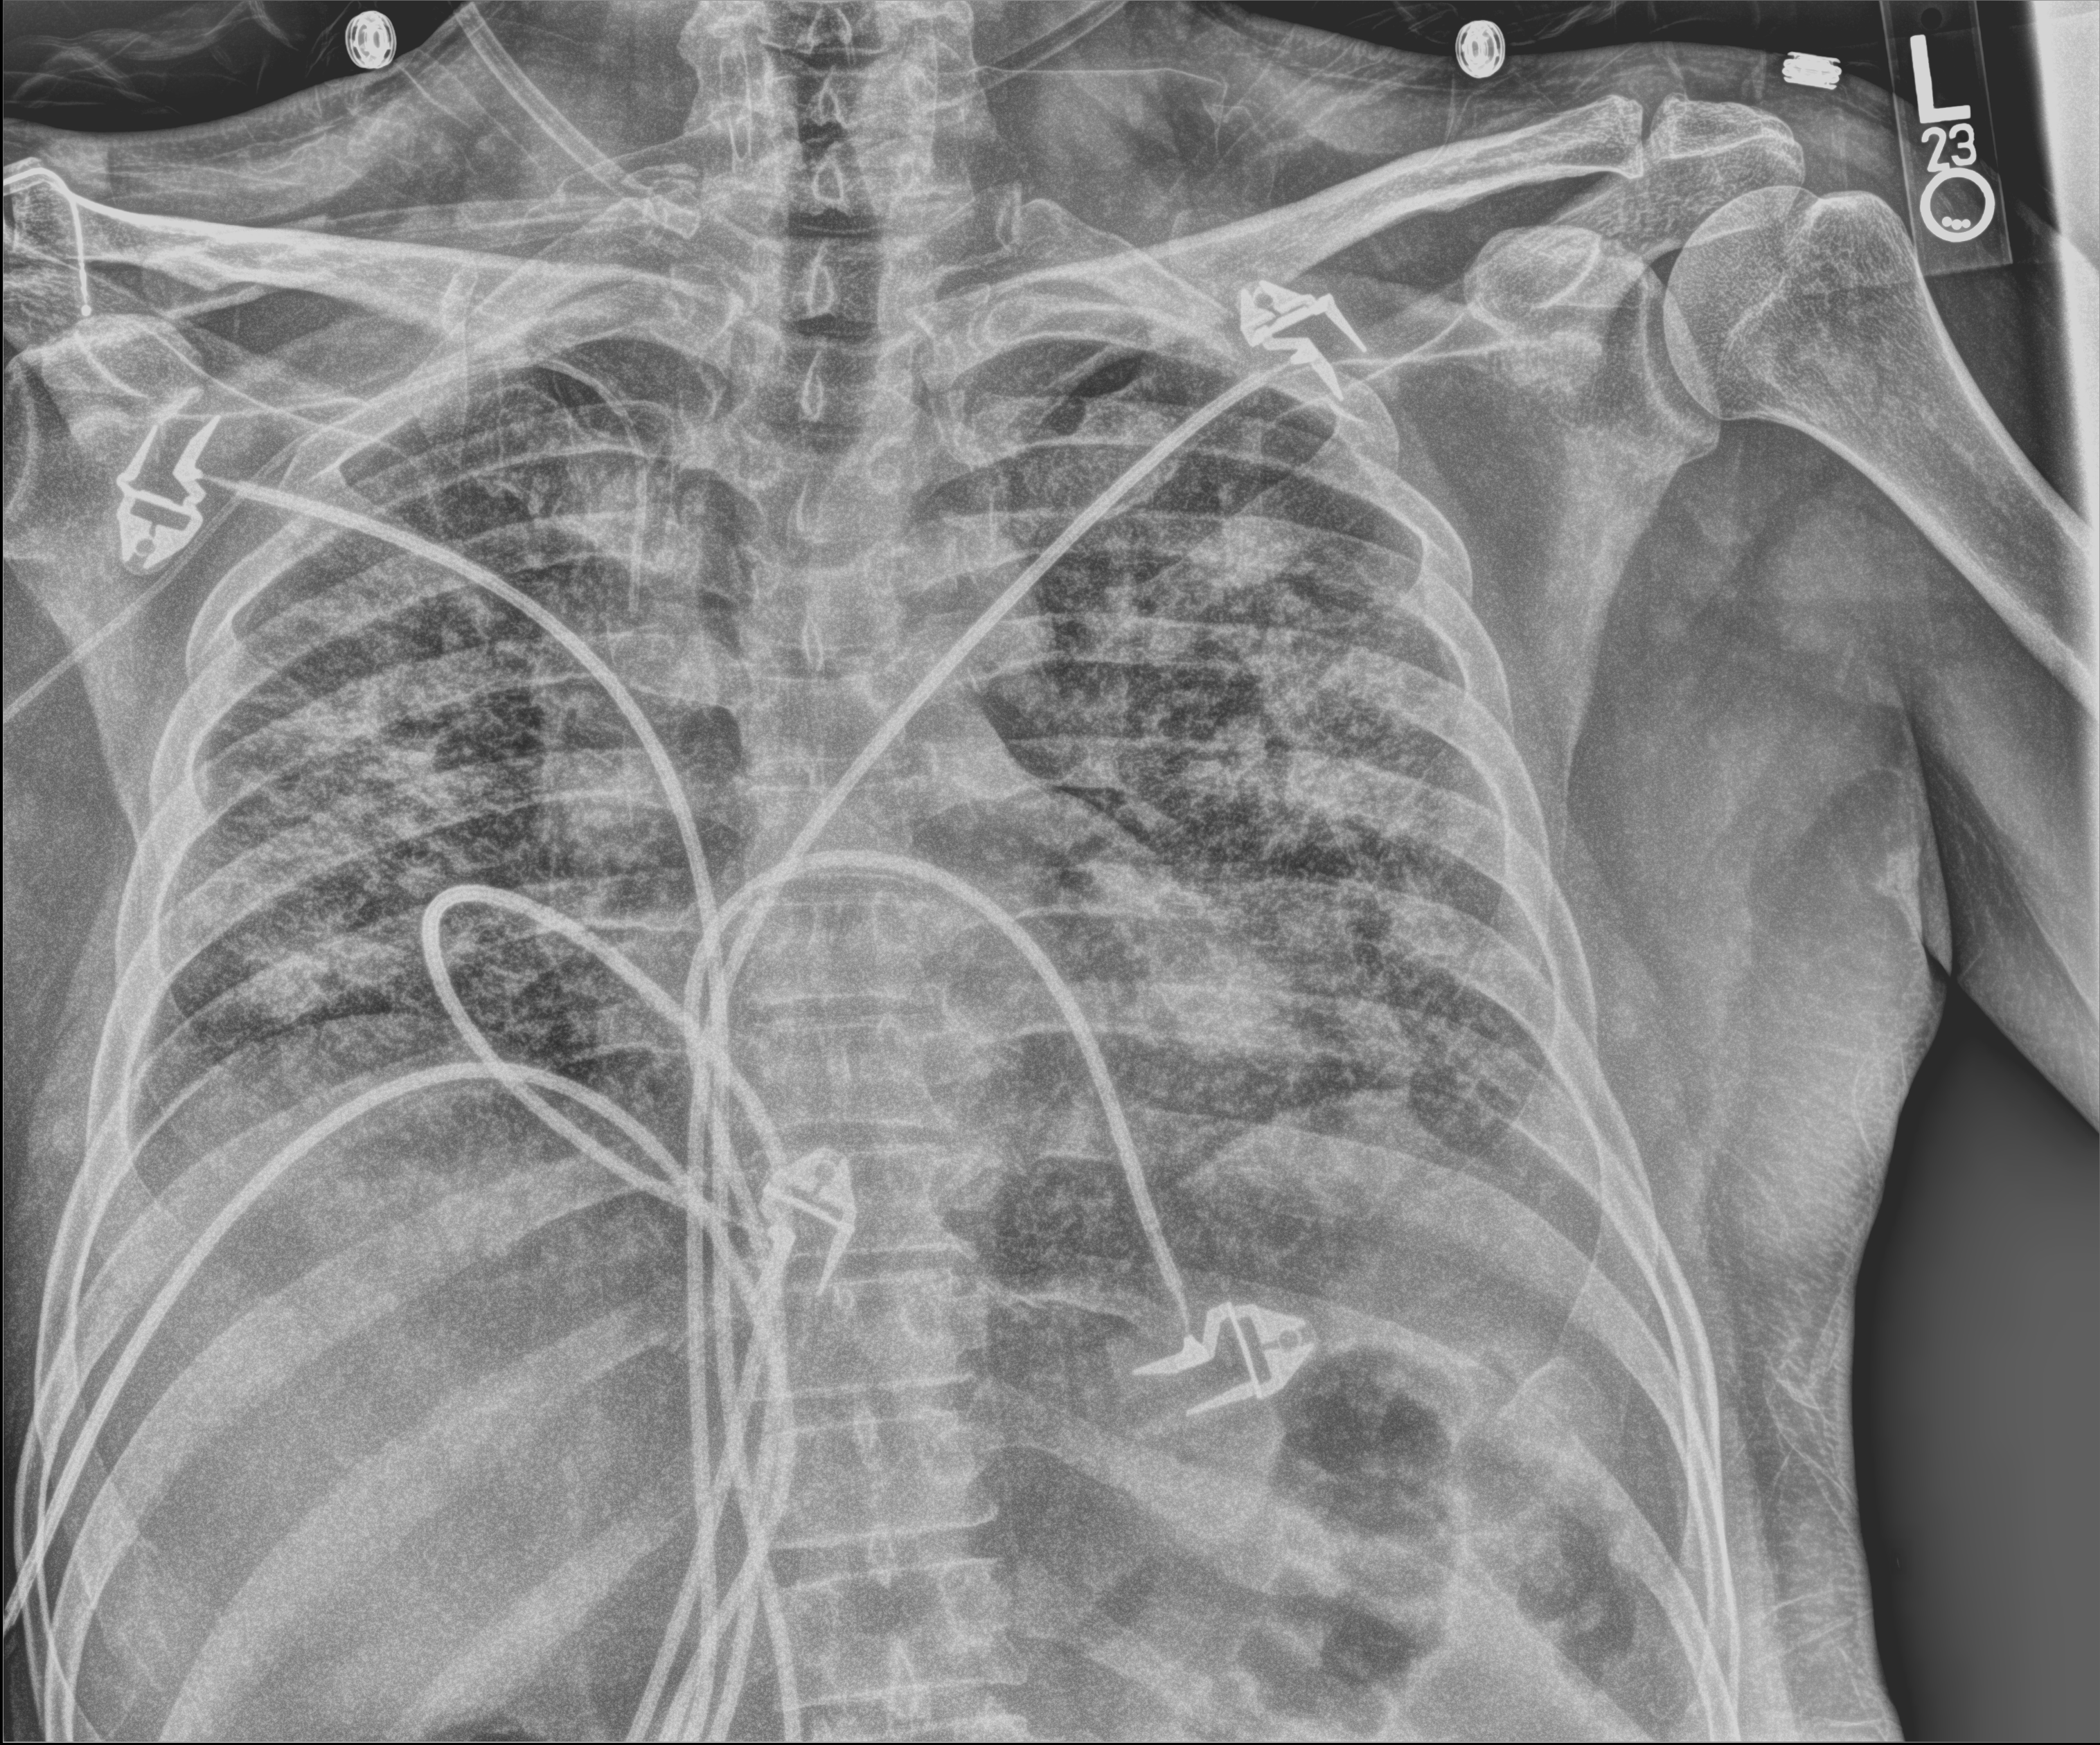
Portable chest radiograph, anteroposterior (AP) projection. Patient hospitalised with COVID-19; male, aged 18–59 years.
From the hospital-stay record, not from the radiograph (when in the stay this image was taken is not recorded):
- length of hospital stay: 77 days